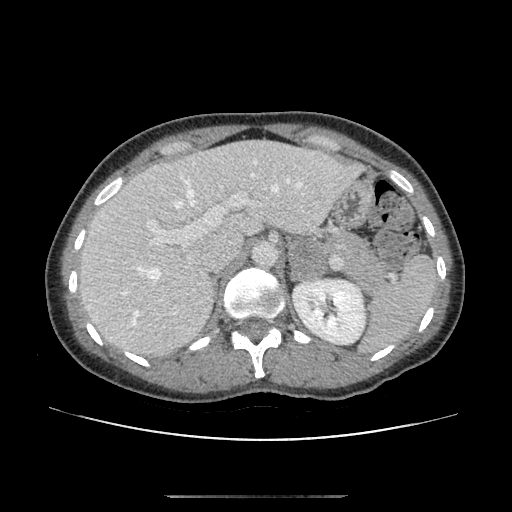
Contrast-enhanced abdominal CT, one axial slice. Slice 72 of 179 in the series (ordered by position). 120 kVp. Soft-tissue window (W 400 / L 40 HU). 512 × 512 image matrix, field of view 360 × 360 mm. Female patient, age 51 years. From the clinical record (not read from this slice): diagnosis: adrenocortical carcinoma; tumour side: left adrenal; tumour size at pathology: 3.5 cm; Ki-67 index: 45 %; stage (as recorded): 1.
Annotated regions visible in this slice (semi-automatic segmentation, software-assisted and operator-edited):
- mass: bounding box [x1, y1, x2, y2] px = [292, 240, 325, 280]